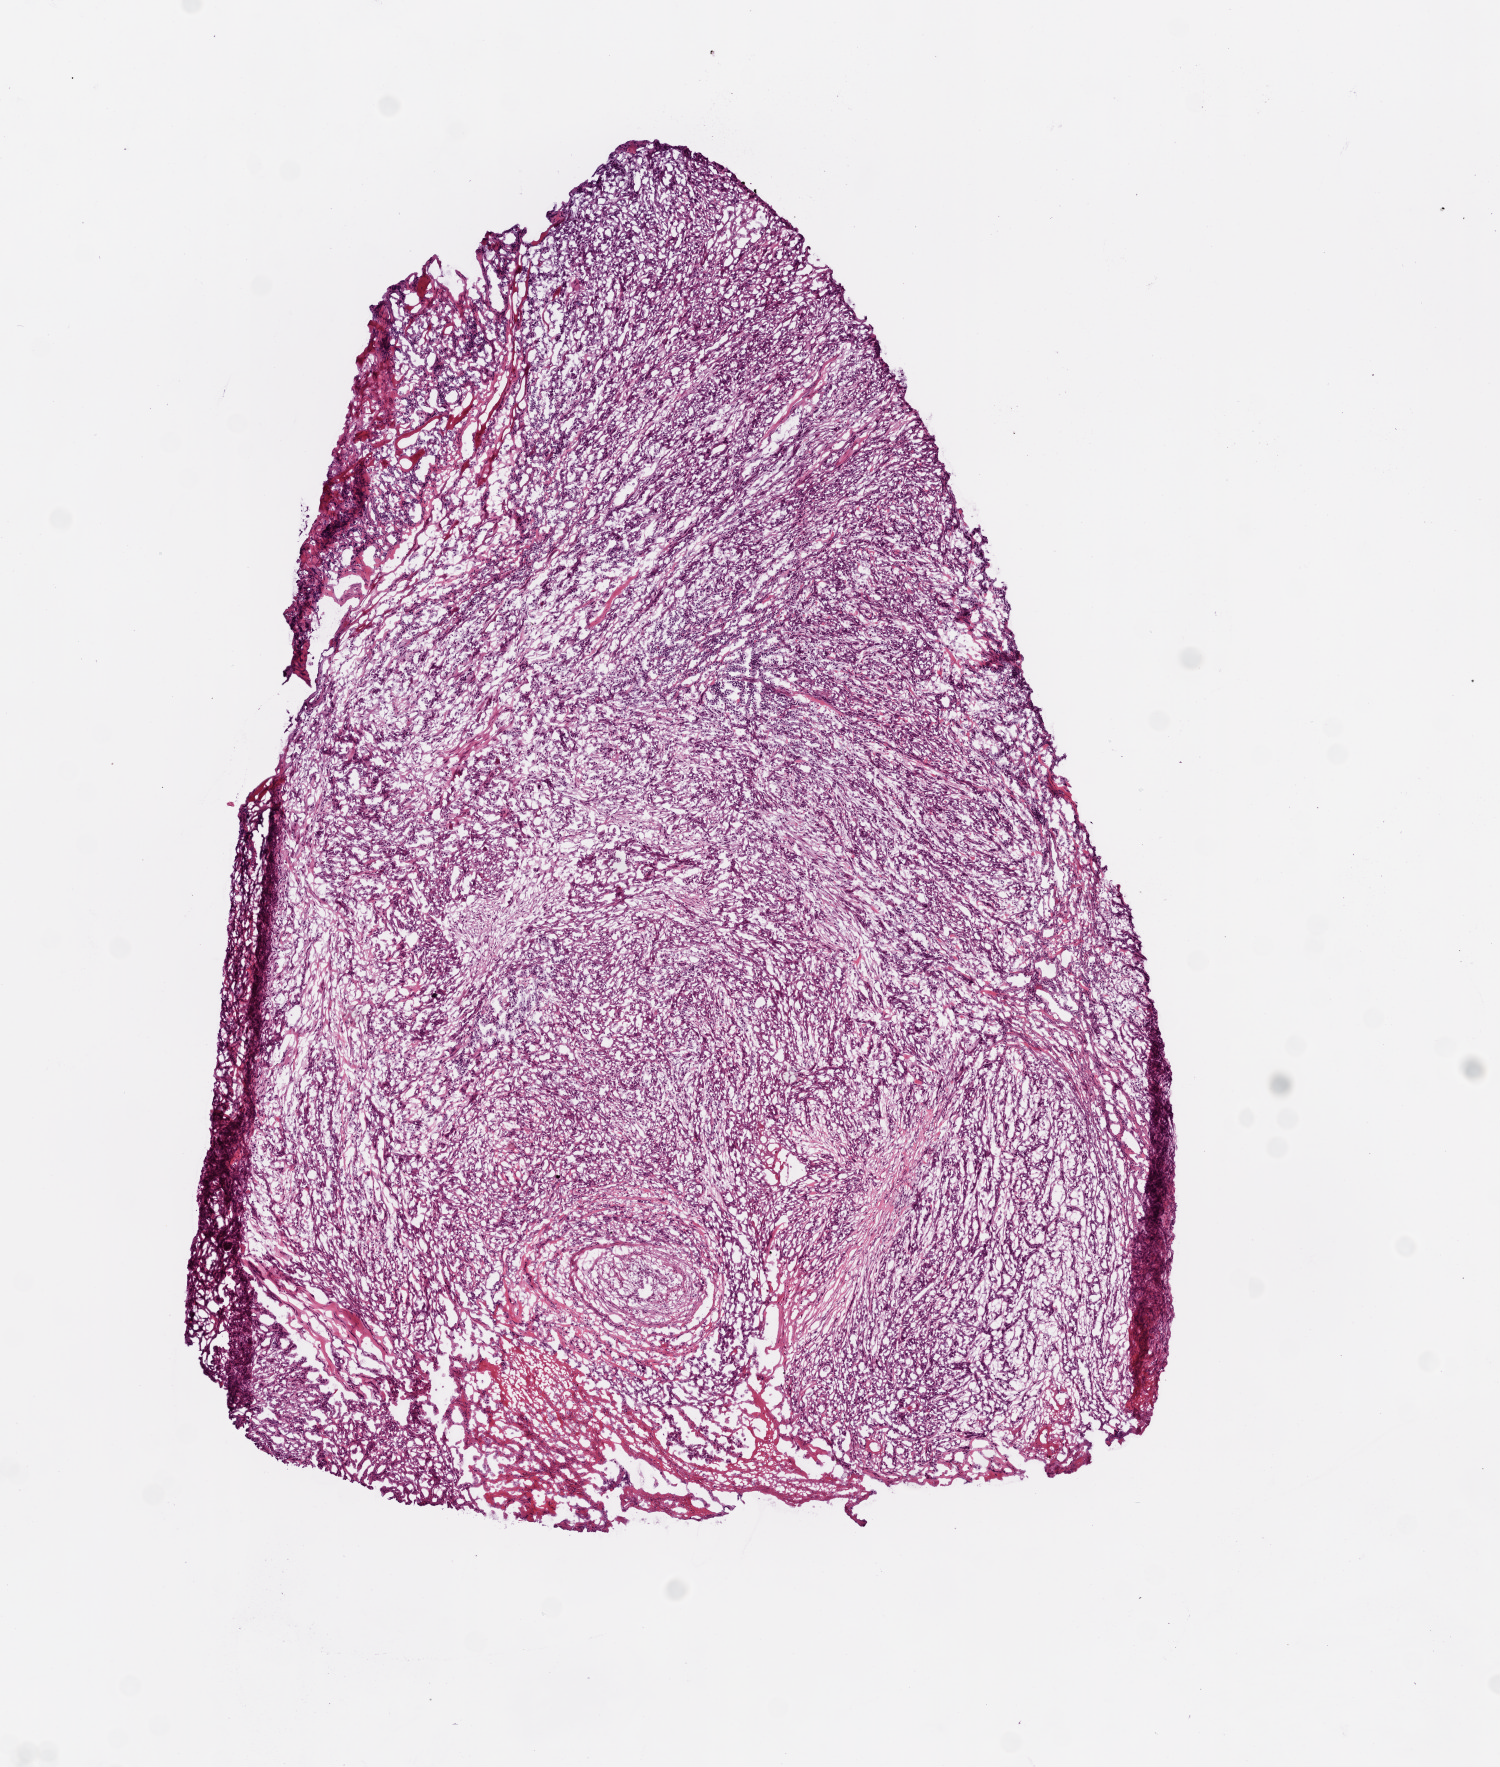
Digitized H&E tissue section (whole slide), whole scanned area (about 6.0 x 7.1 mm) shown as a low-resolution overview; frozen section; primary tumour sample from the head and neck. Male, age 48 years at initial diagnosis. Histologic grade: G3 (poorly differentiated). Composition of this section per pathologist review: tumour cells 90%, tumour nuclei 70%, normal cells 0%, stromal cells 10%, necrosis 0%.
Diagnosis: Squamous cell carcinoma, NOS (larynx, NOS). AJCC pathologic stage: IVB (6th edition).